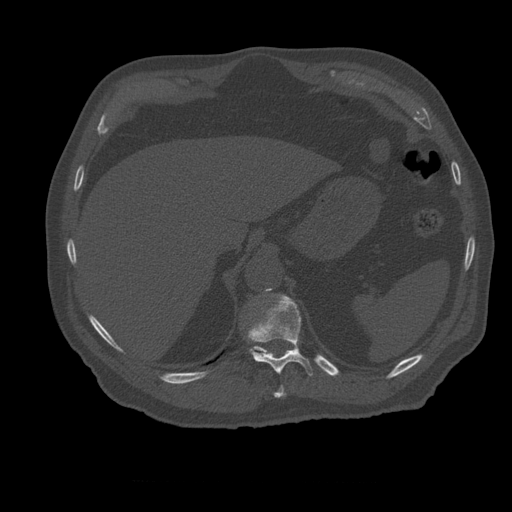
CT including the spine, one axial slice. Position 280 of 399 along the scan axis. 120 kVp. Bone window (W 1800 / L 400 HU). 1.25 mm slice thickness. 512 × 512 image matrix, field of view 407 × 407 mm. Patient age 73 years. From the clinical record (not read from this slice): primary cancer: prostate.
Outlined on this slice (semi-automatic segmentation, software-assisted and operator-edited):
- T10 vertebra: box from (x=274, y=386) to (x=286, y=398) px
- T11 vertebra: (x=248, y=295)–(x=314, y=376)
- T12 vertebra: (x=246, y=302)–(x=288, y=357)